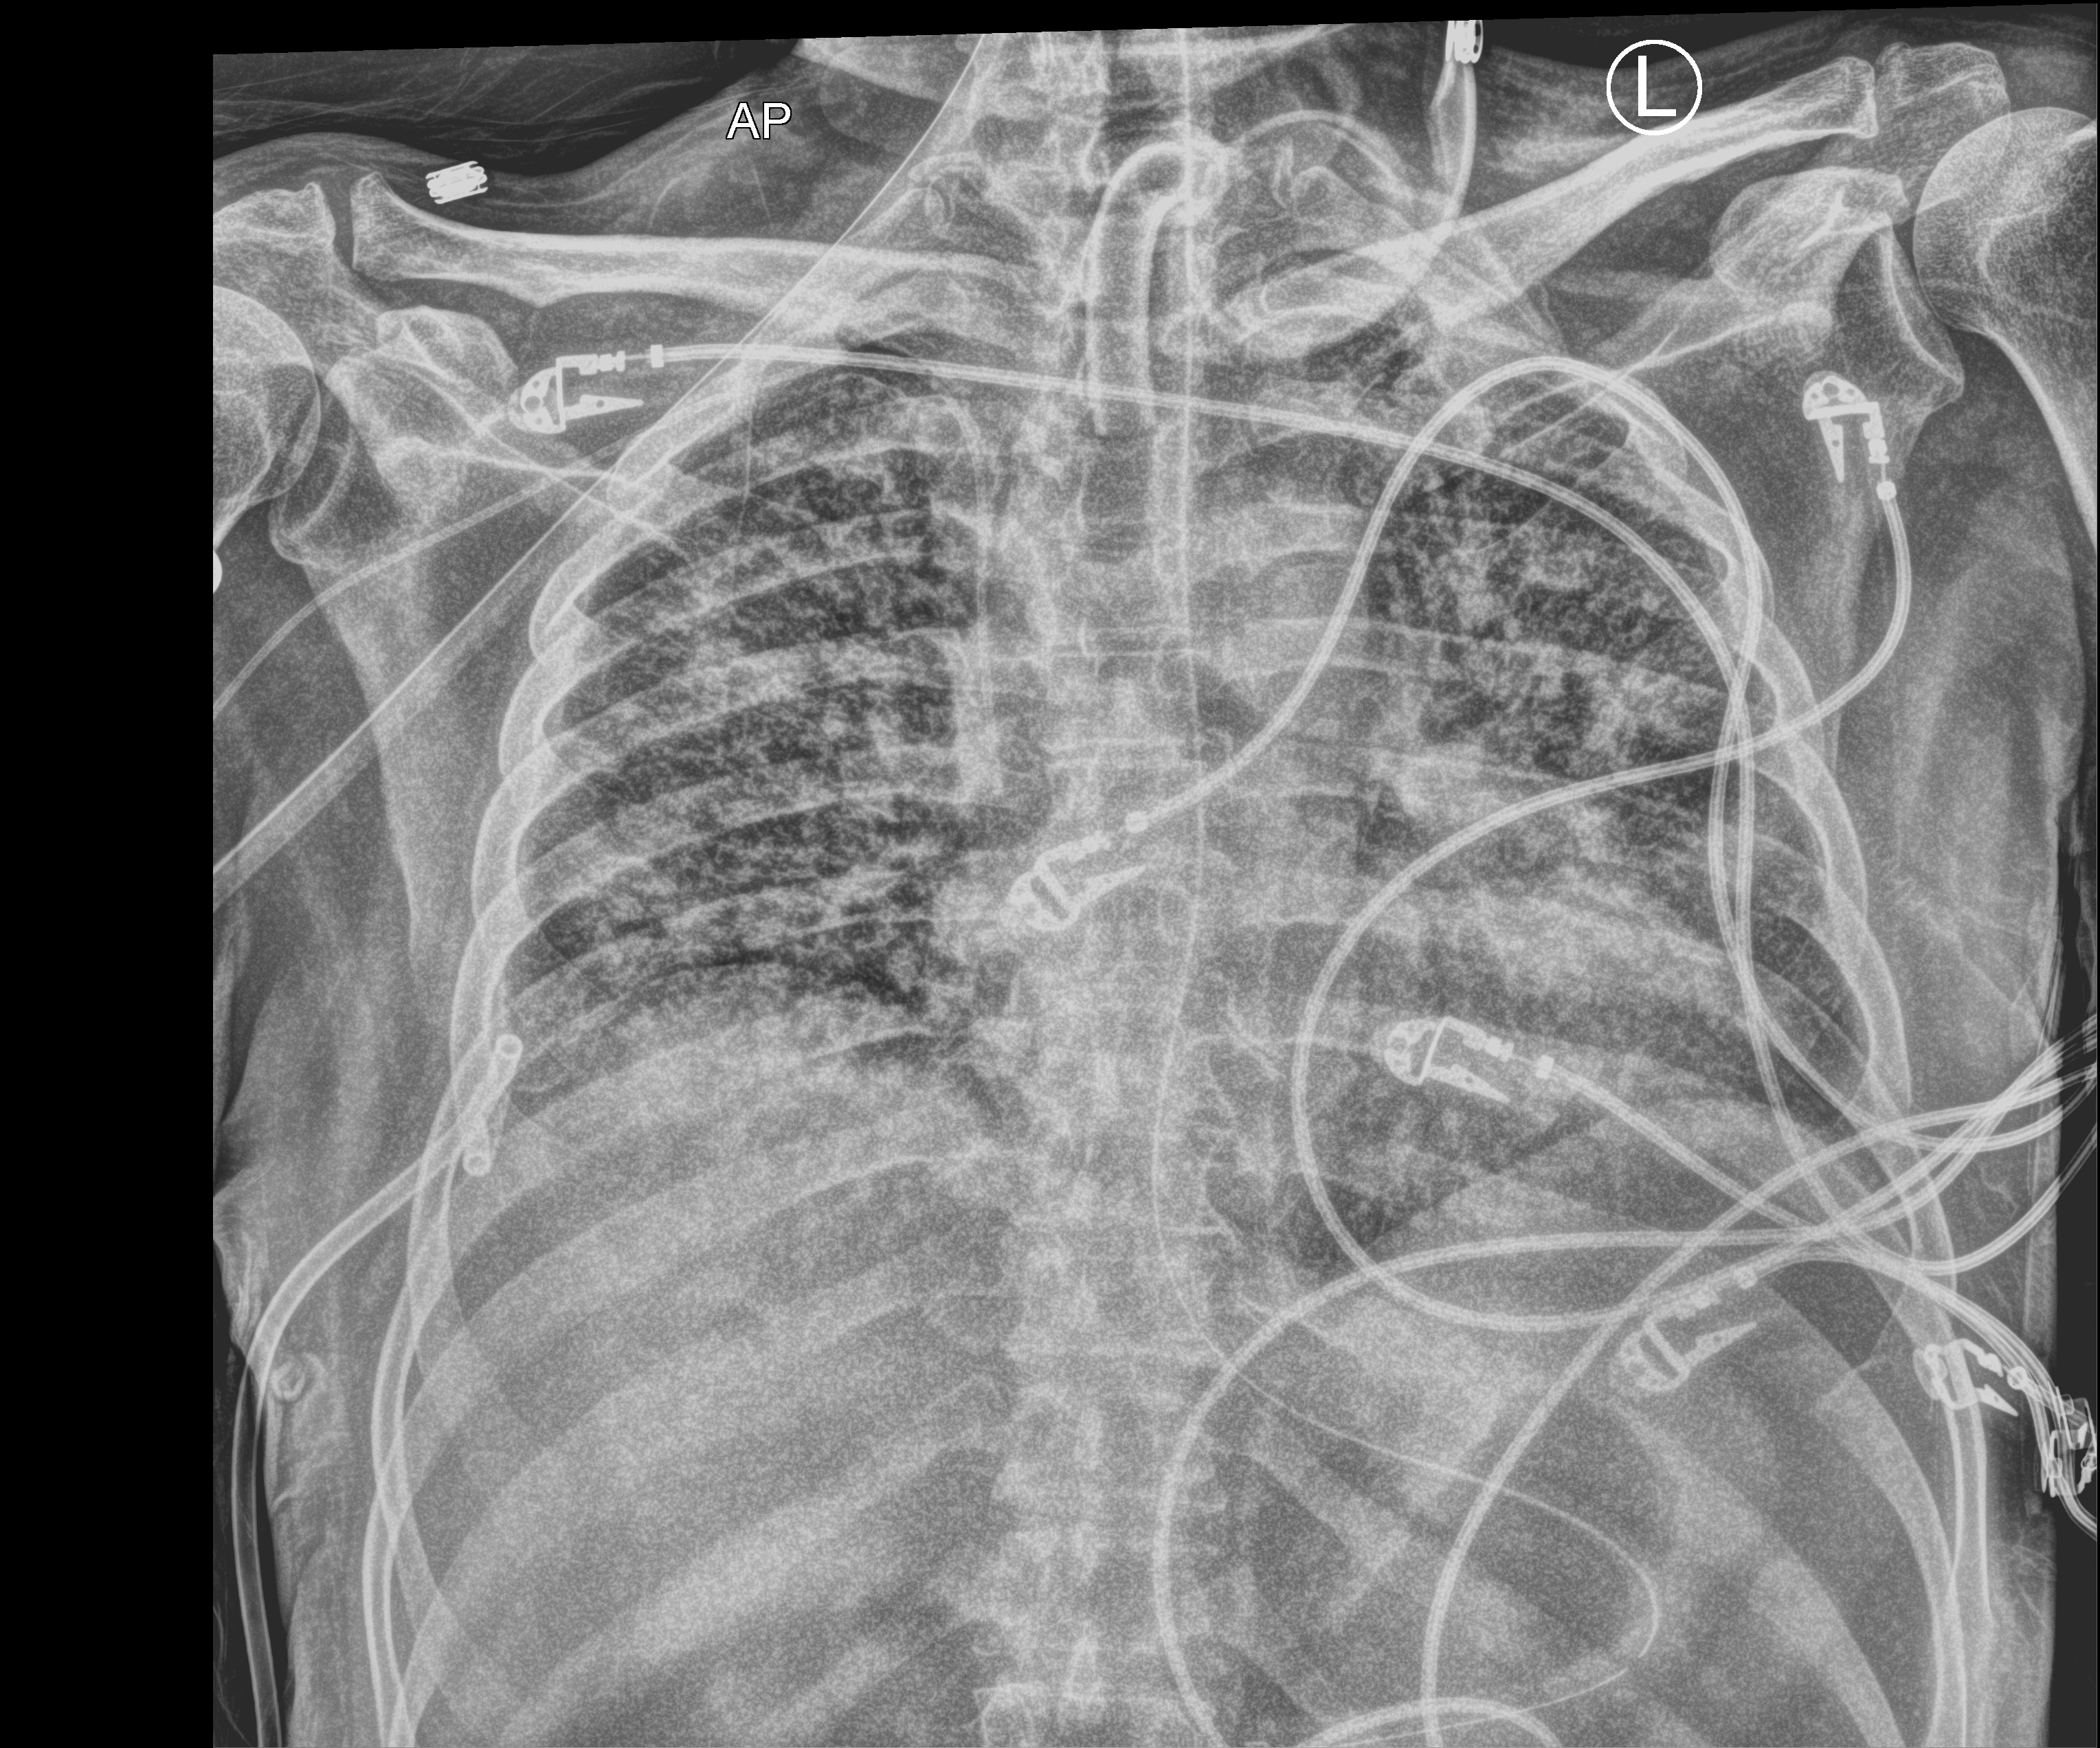
Chest X-ray (portable); anteroposterior (AP) projection. Male patient hospitalised with COVID-19, age 18–59 years.
Hospital-stay facts (about this admission, not read from this image; timing relative to this image not recorded): chronic kidney disease (admission record): no.